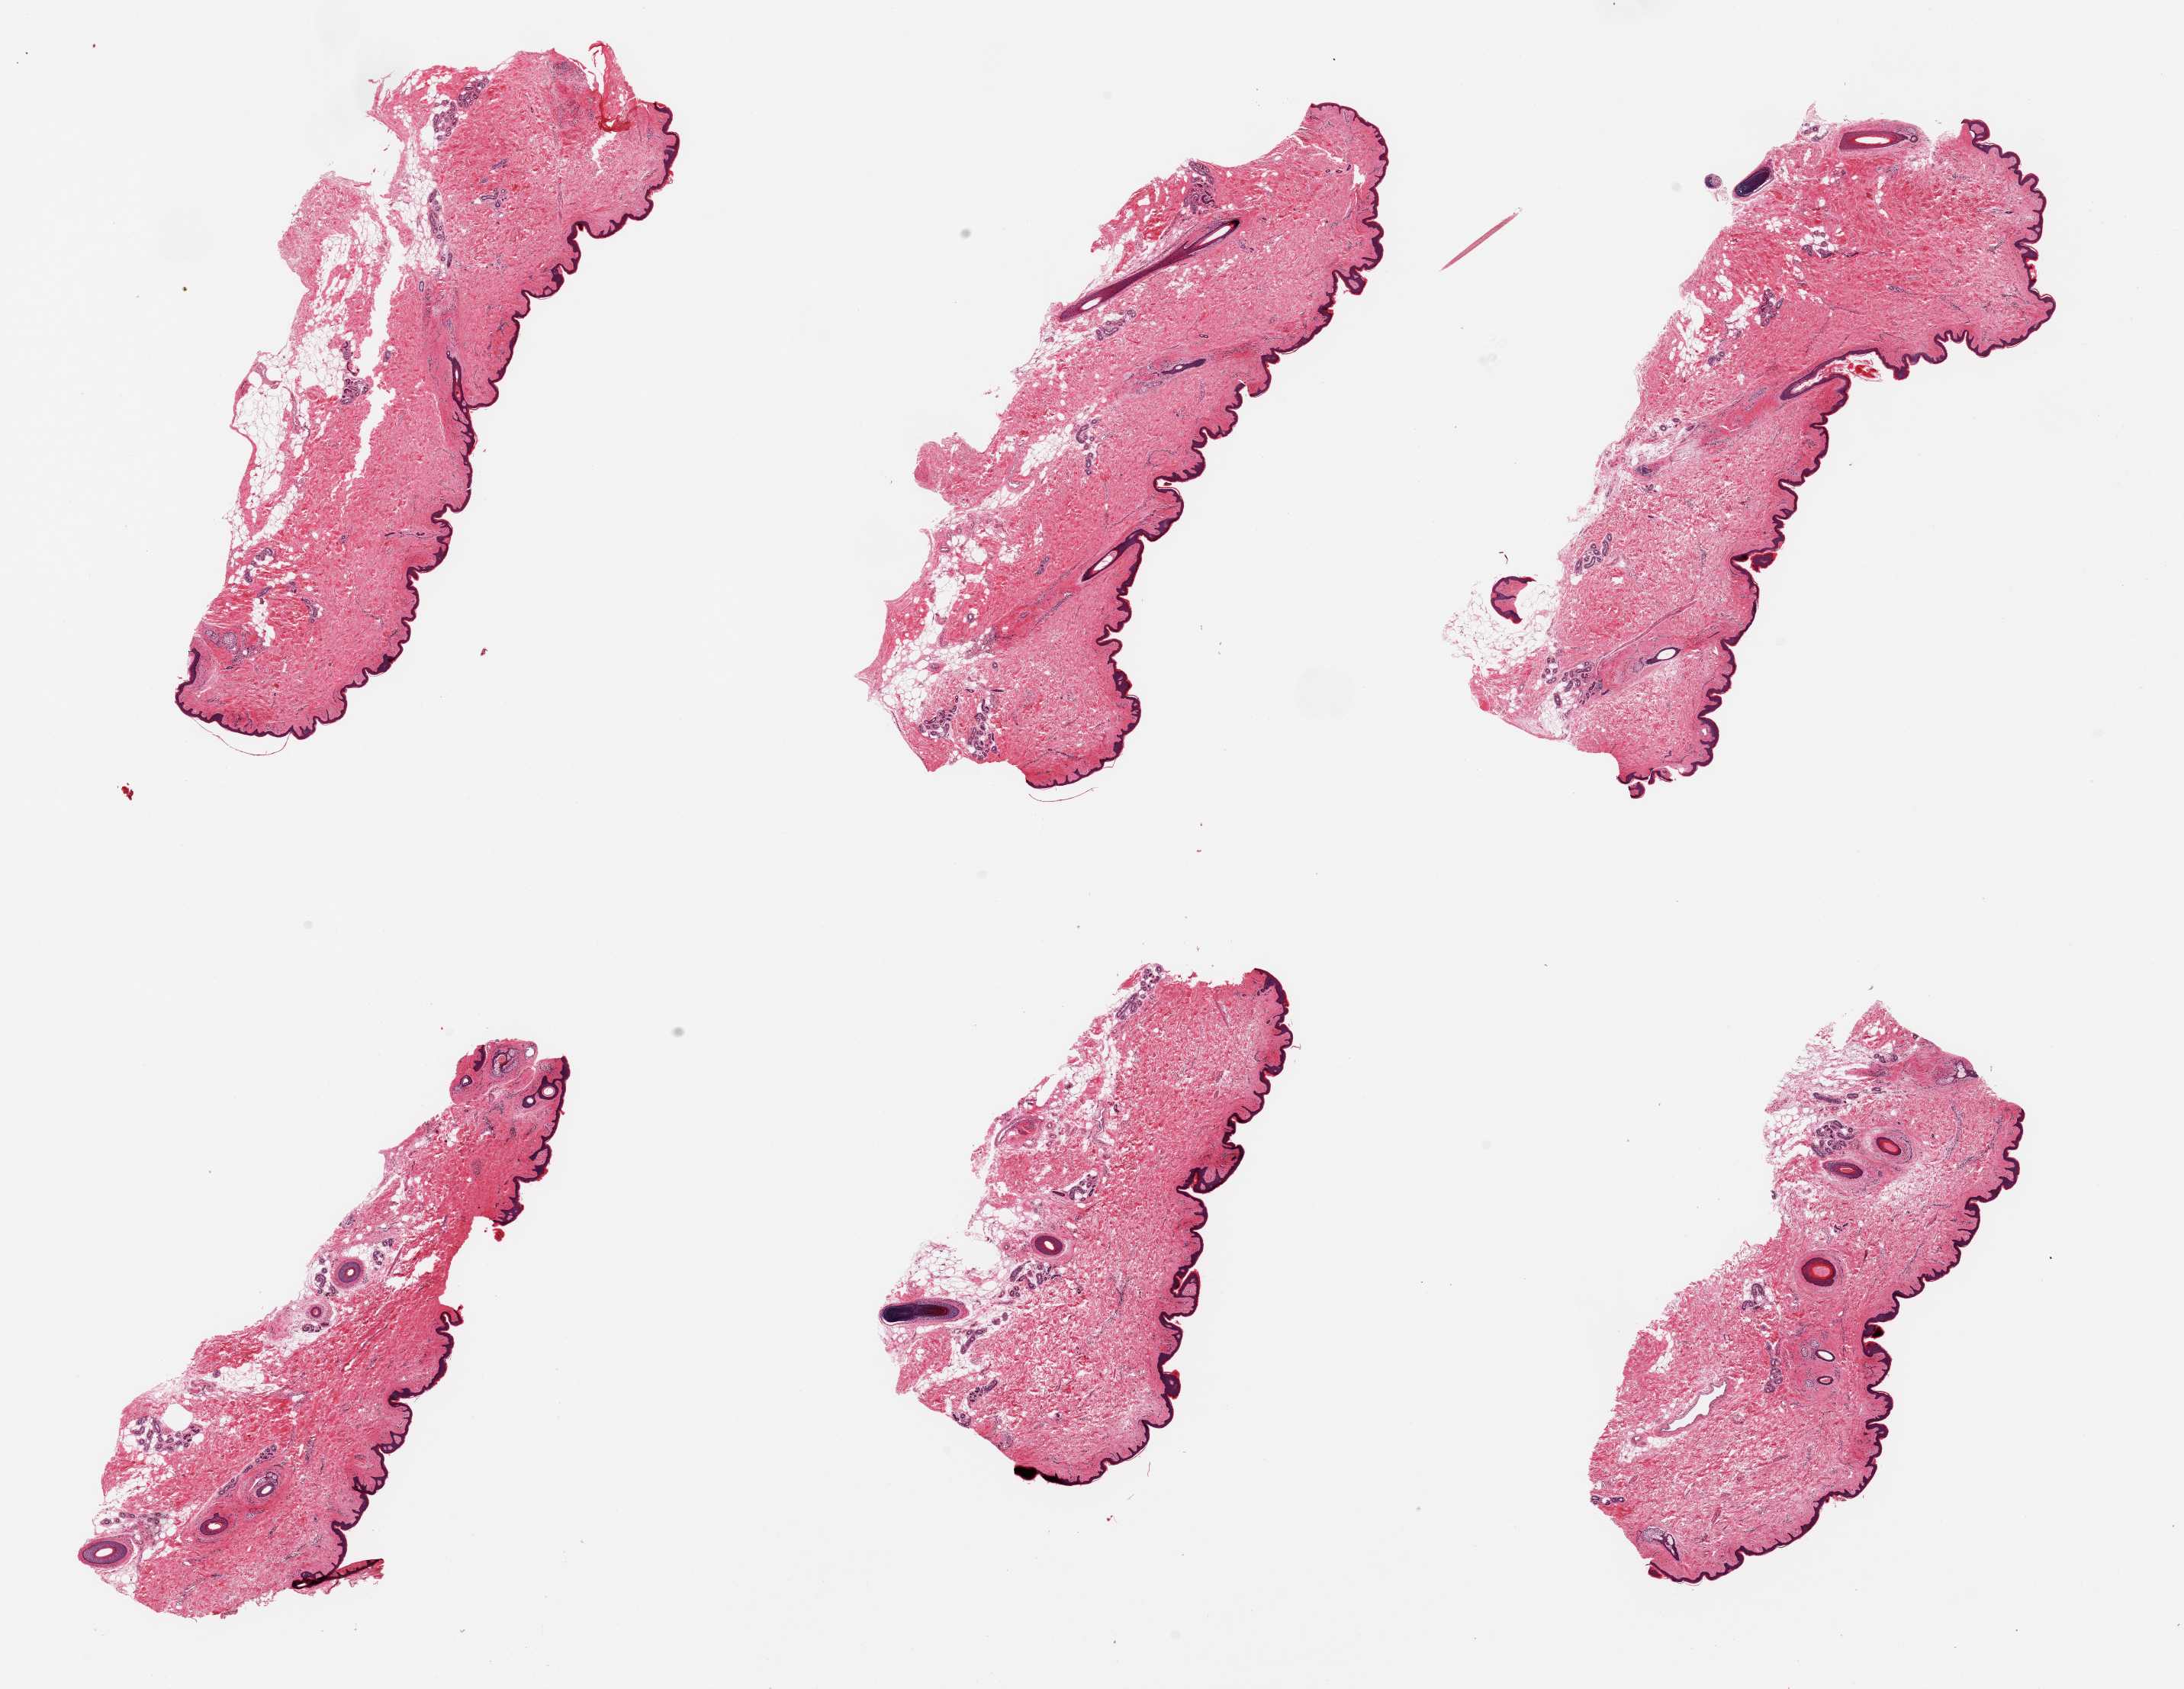
Whole-slide image, haematoxylin and eosin stain, brightfield — a low-resolution overview of the entire scanned area, about 22.6 x 17.5 mm (slide scanned at 20x). PAXgene-fixed paraffin-embedded (PFPE) section. Section of skin of suprapubic region (target tissue). Tissue donor sample.
Reviewer comment on this tissue sample: 6 pieces, minimal adherent dermal fat; squamous epithelium is ~30-40 microns.